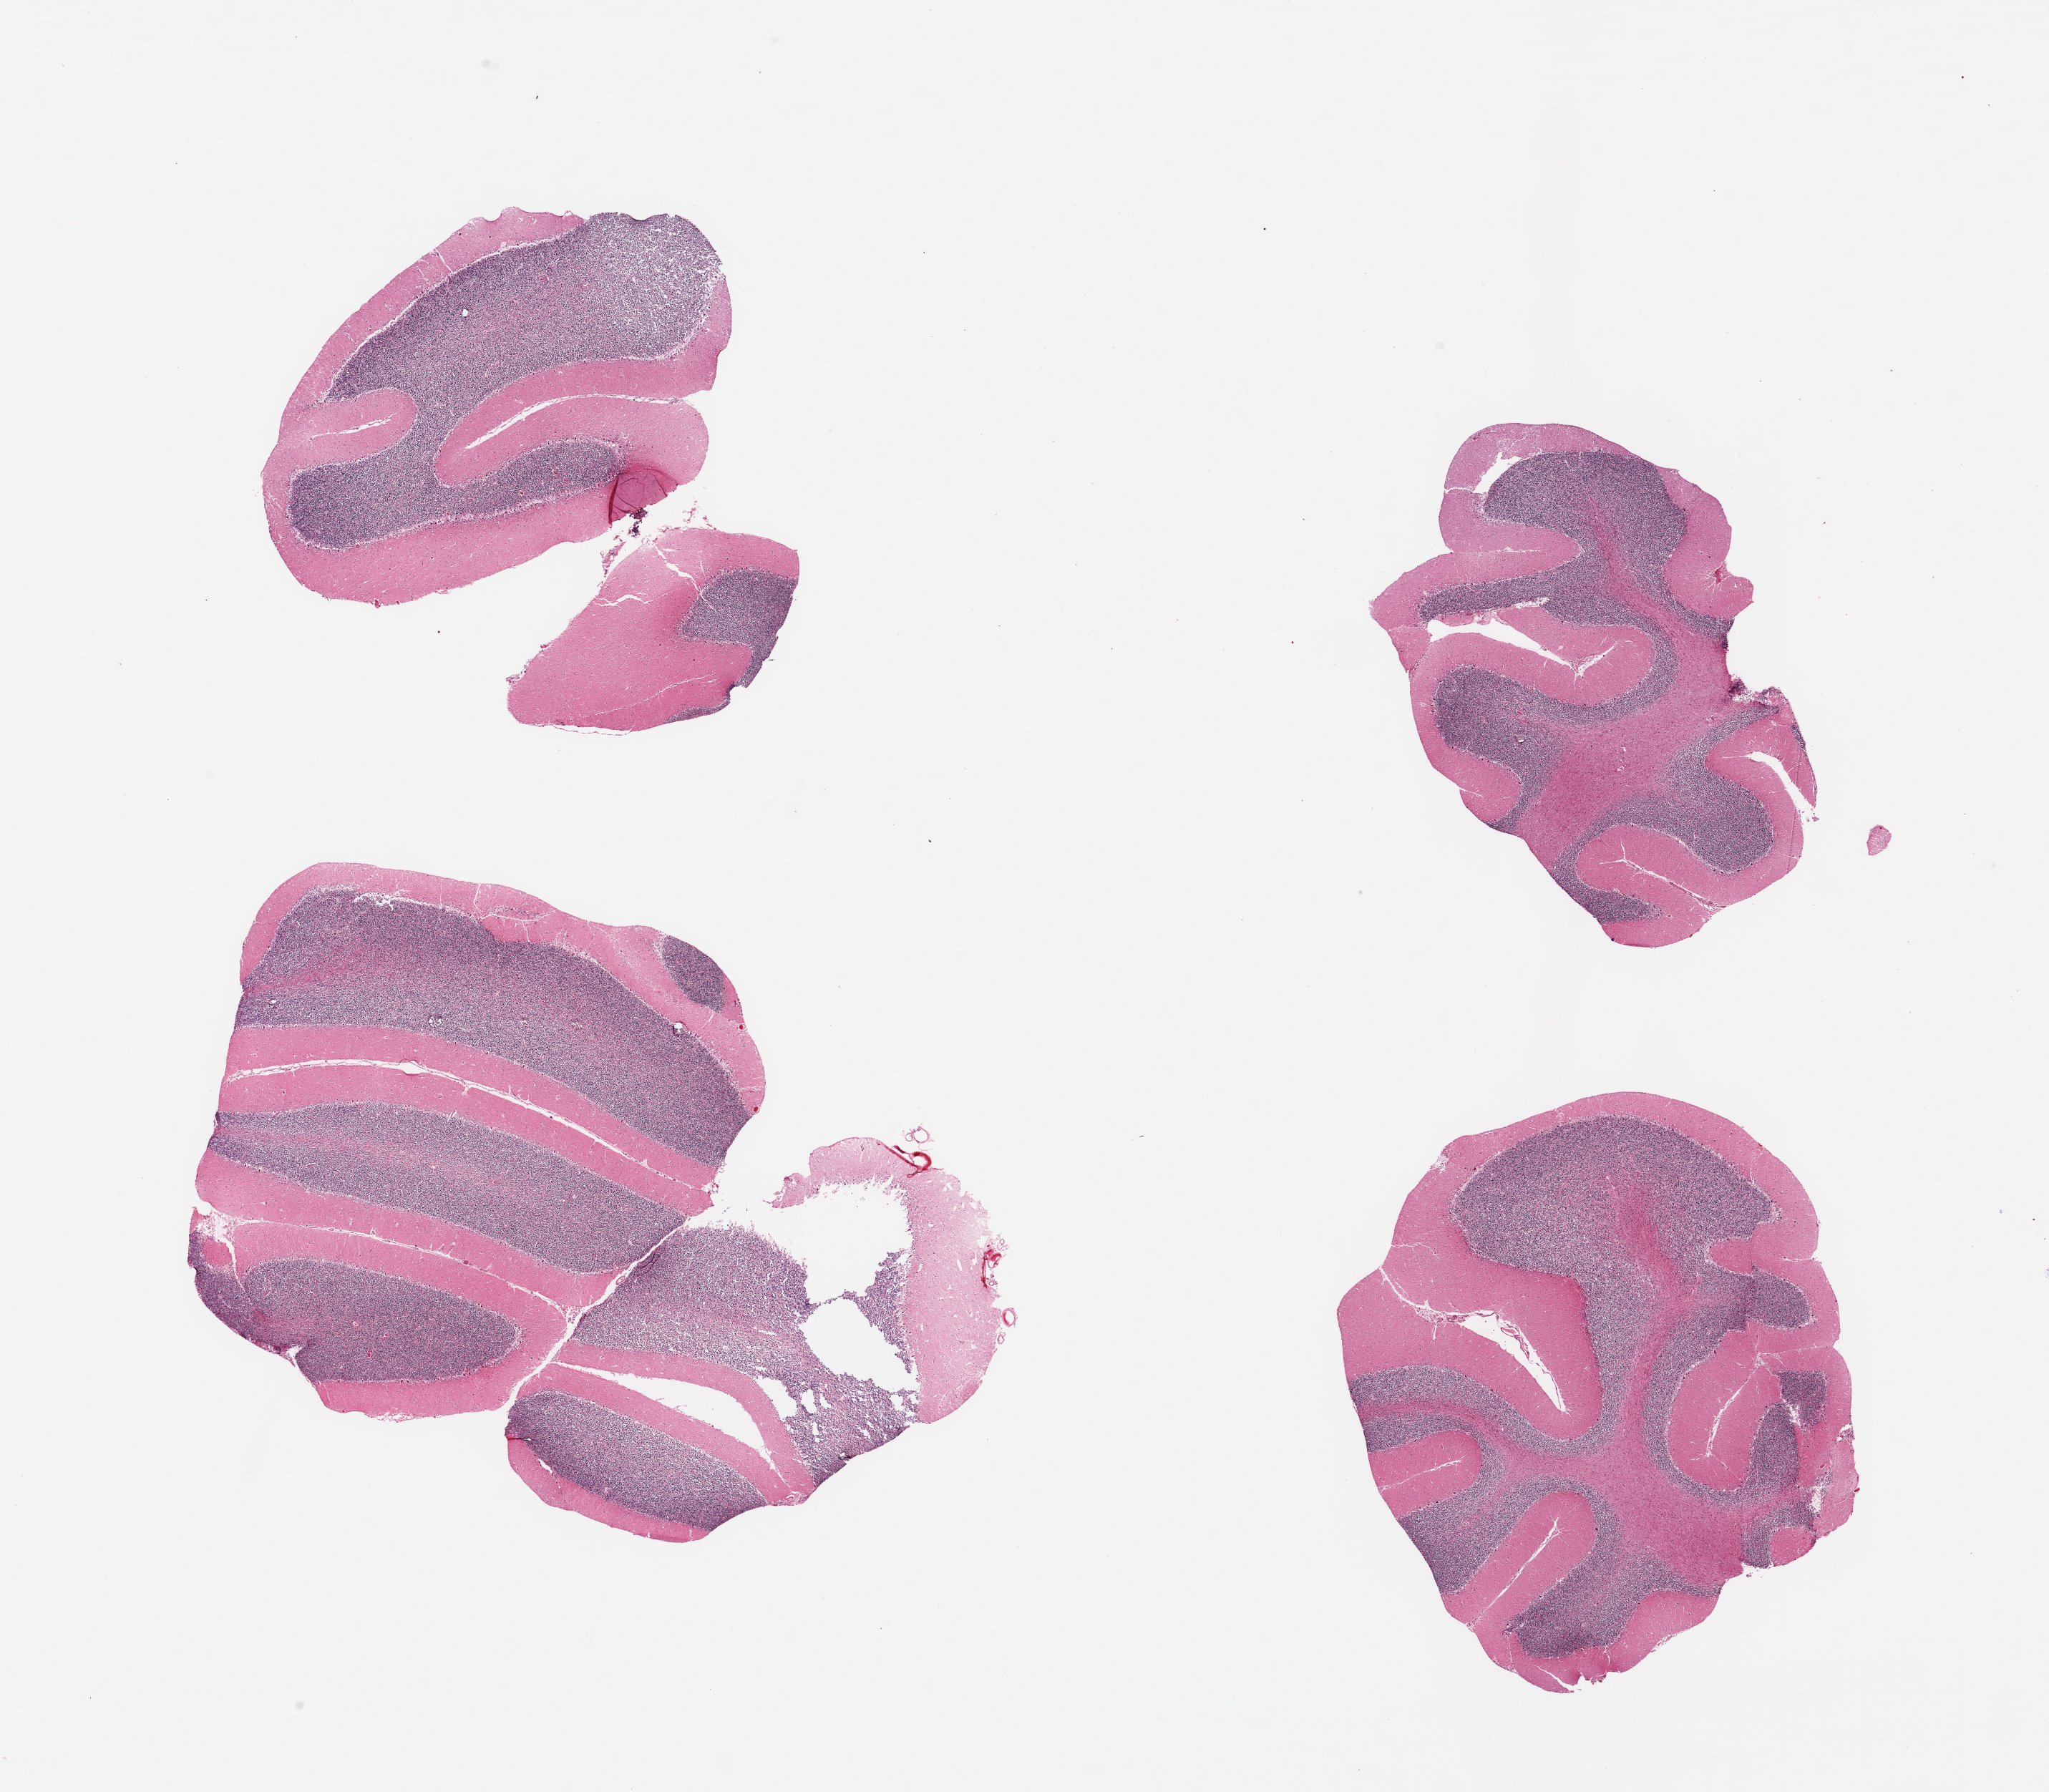
Digitized hematoxylin and eosin (H&E)-stained section, brightfield — whole scanned area (about 22.6 x 19.8 mm) shown as a low-resolution overview; PAXgene-fixed paraffin-embedded (PFPE) section; sampled site (target tissue): cerebellum; tissue donor sample. Donor sex: female.
Review note (as recorded): 4 partly fragmented pieces.